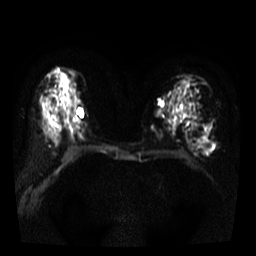
Breast MRI, one axial slice. Slice 20 of 38 in the series (ordered by position). Diffusion-weighted series; image 2 of 4 stored at this slice position (different b-values; order by instance number). 3 T. 256 × 256 image matrix. Female patient.
Outlined on this slice (outlined manually by an expert reader):
- tumour on diffusion-weighted imaging: bounding box [x1, y1, x2, y2] px = [199, 137, 211, 152]